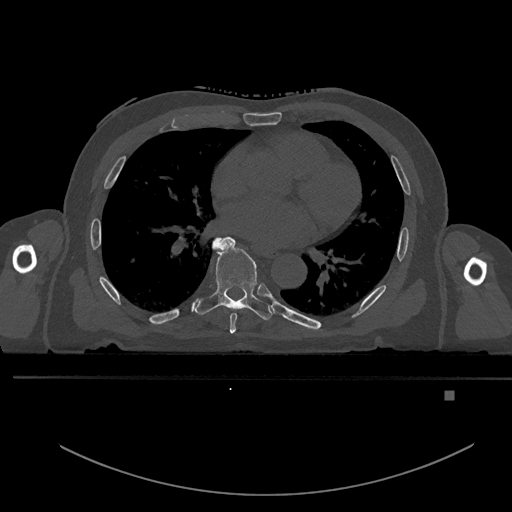
CT including the spine, one axial slice; slice 266 of 969 in the series (ordered by position); bone window (W 1800 / L 400 HU); 0.5 mm slice thickness; 512 × 512 image matrix, field of view 456 × 456 mm. Male patient, age 82 years. From the clinical record (not read from this slice): primary cancer: prostate.
Annotated regions visible in this slice (semi-automatic segmentation, software-assisted and operator-edited):
- T6 vertebra: bounding box <229,312,237,334> (left, top, right, bottom; pixels)
- T7 vertebra: <193,237,272,320>